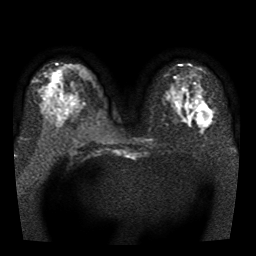
Breast MRI, one axial slice; slice 19 of 41 in the series (ordered by position); diffusion-weighted series; image 2 of 3 stored at this slice position (different b-values; order by instance number); 1.5 T; 5 mm slice thickness; 256 × 256 image matrix, field of view 330 × 330 mm. Female patient.
Structures marked on this image (expert manual segmentation):
- tumour on diffusion-weighted imaging: bounding box <198,105,211,123> (left, top, right, bottom; pixels)